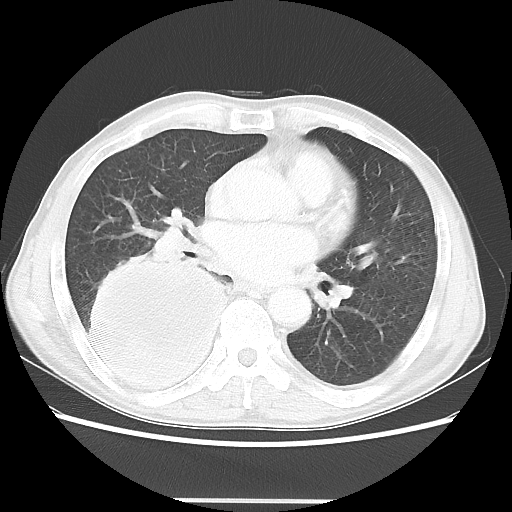
Chest CT, one axial slice. Lung window (W 1500 / L -600 HU). 512 × 512 image matrix, field of view 361 × 361 mm. Patient: male, 66 years. From the clinical record (not read from this slice): clinical TNM (as recorded): T4 N1 M1; histopathological grade: G3.
Annotated regions visible in this slice (bounding box drawn by a radiologist):
- lung tumour (recorded histology: small cell carcinoma): bounding box [x1, y1, x2, y2] px = [76, 254, 236, 400]